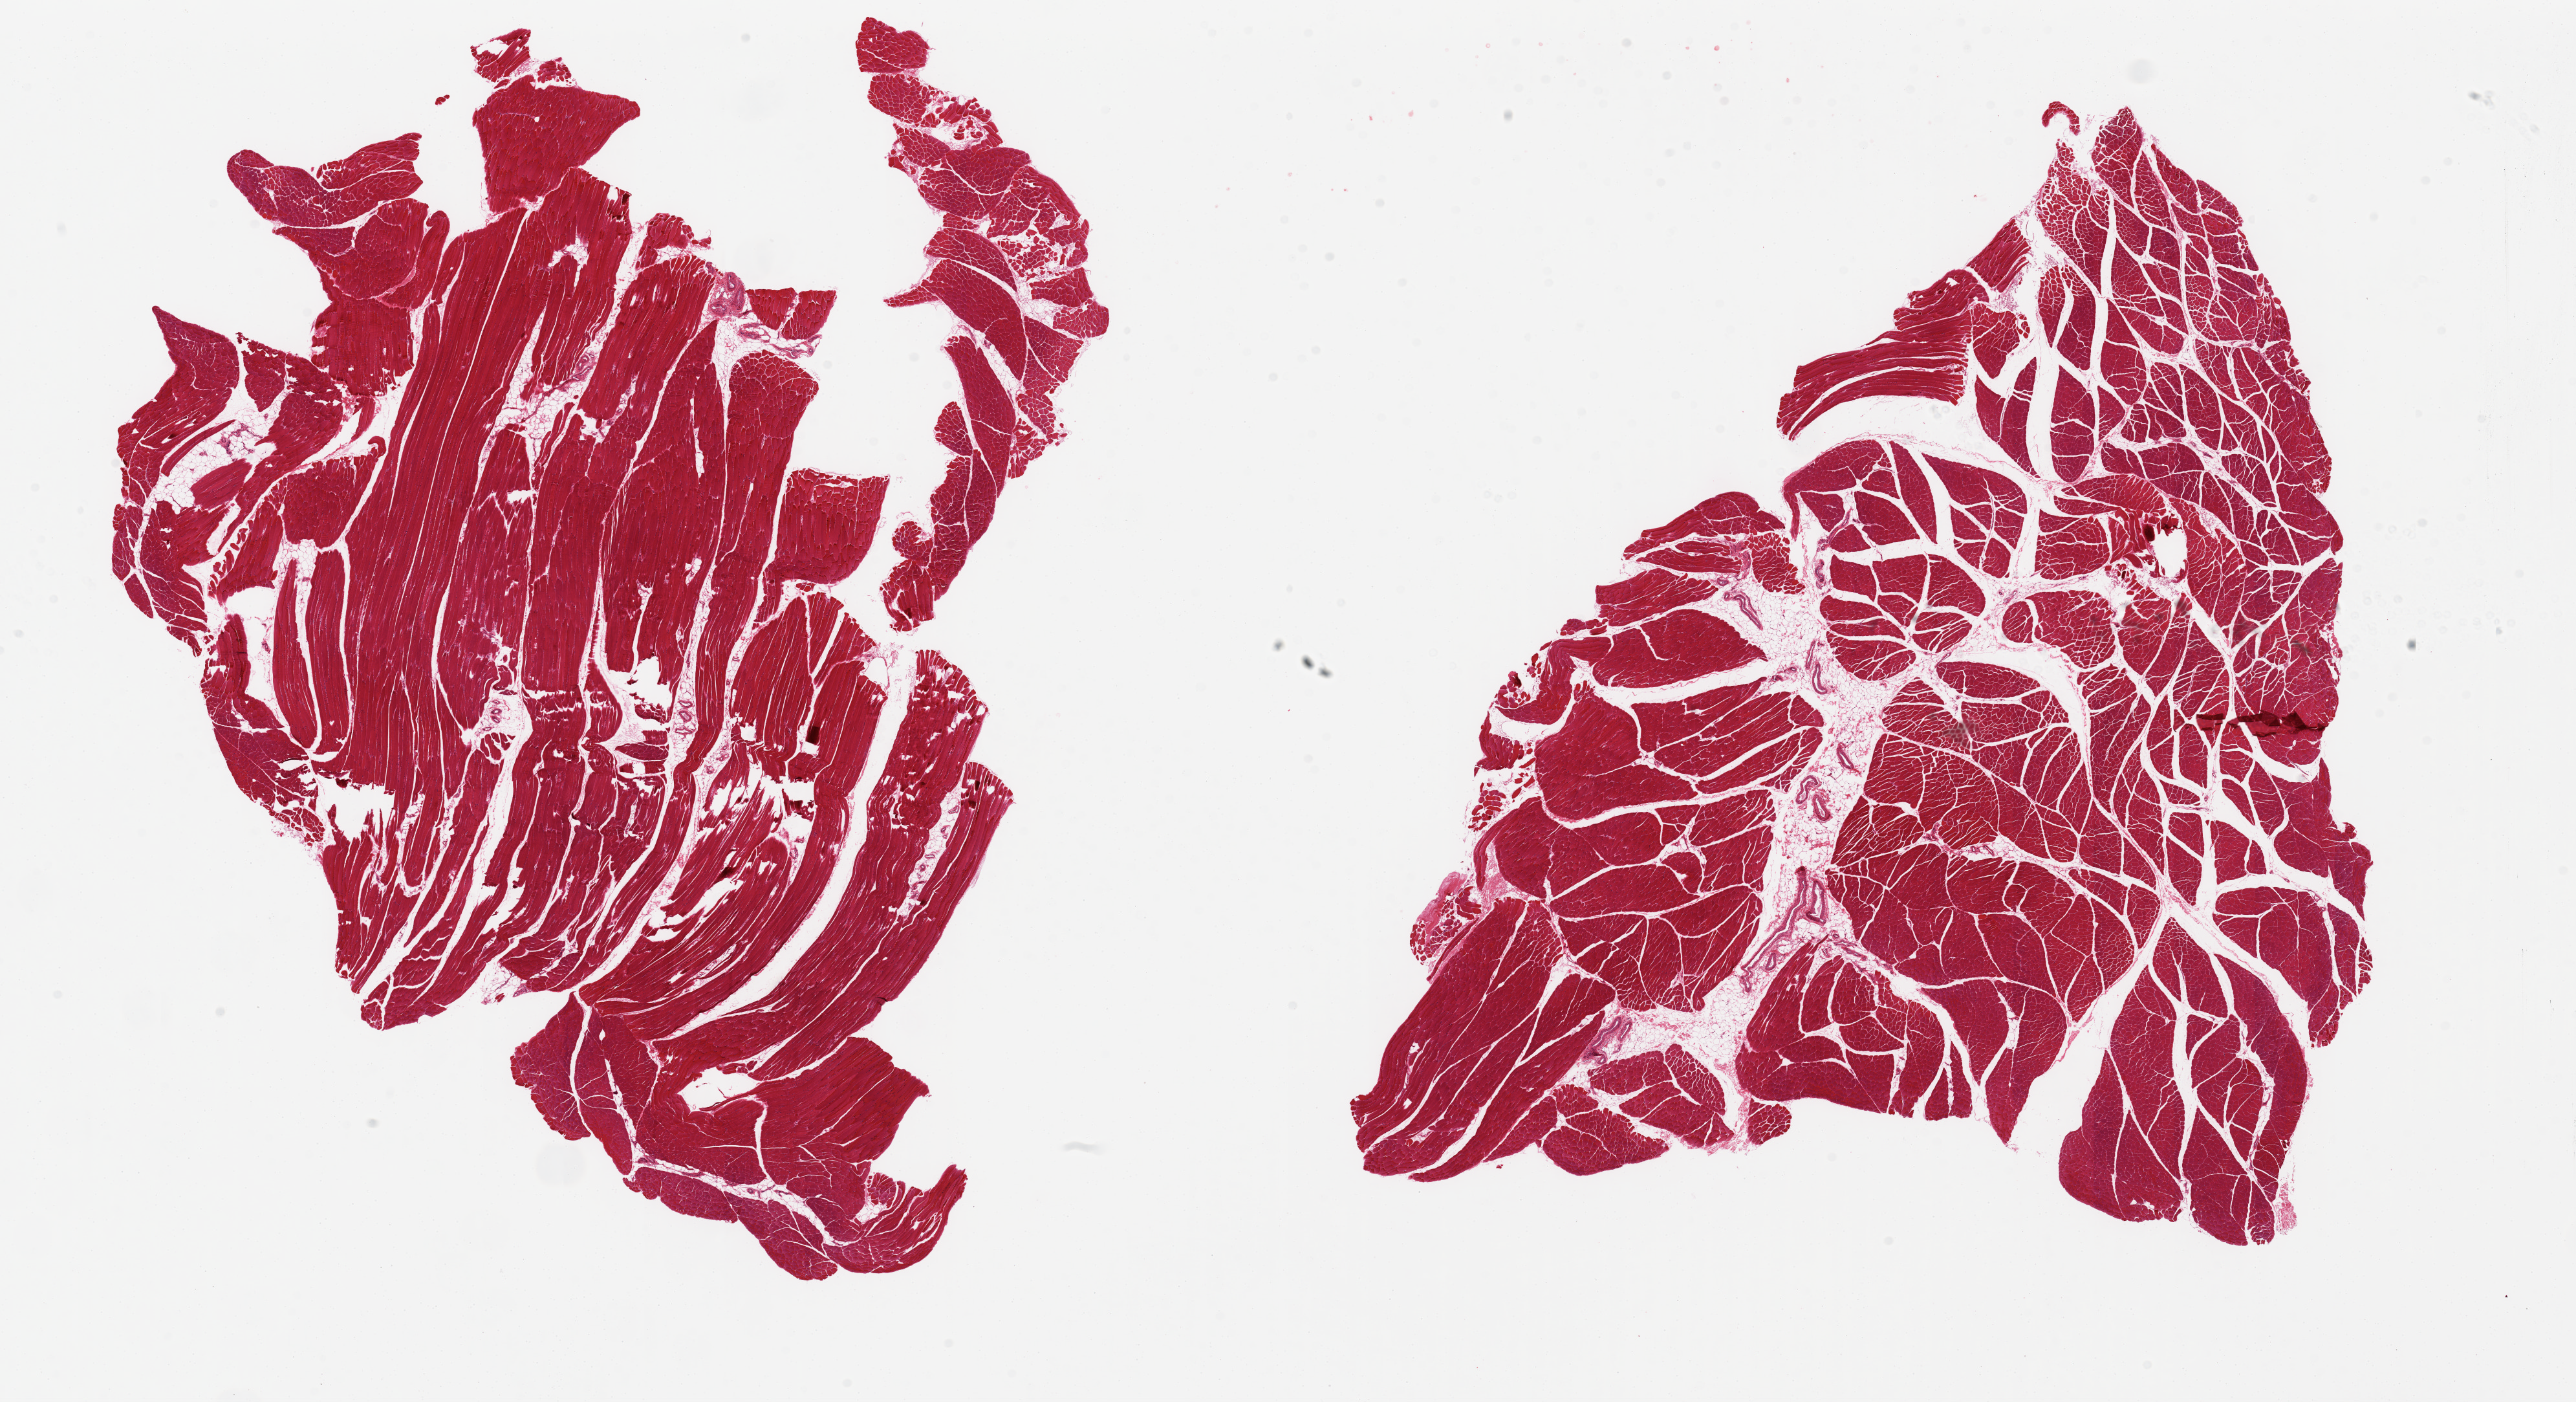
Digitized hematoxylin and eosin (H&E)-stained section — low-resolution overview of the scanned area, about 31.5 x 17.1 mm; PAXgene-fixed, paraffin-embedded tissue; target tissue: skeletal muscle; donor tissue sample. Male donor.
Reviewer comment on this tissue sample: 2 pieces, includes ~10% internal fat.